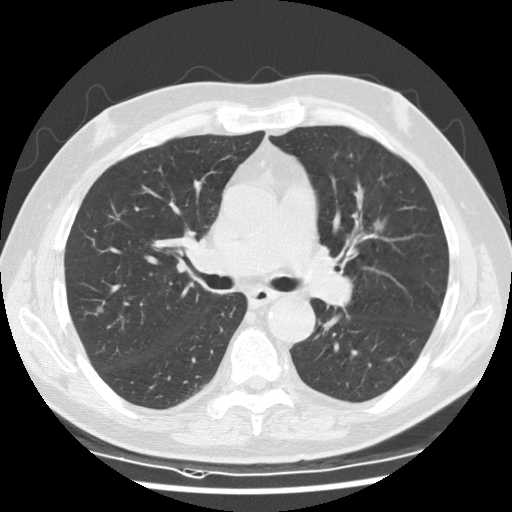
Low-dose screening chest CT, axial slice, baseline annual screen, lung window (W 1500 / L -600 HU). Male participant, aged 73 years at enrolment. Current smoker at enrolment.
Expert-annotated lung lesion, bounding box <332,203,404,254> (left, top, right, bottom; pixels). The exam's reader record, not a measurement of the box and not confirmed to be the same lesion: non-calcified nodule or mass ≥4 mm, right lower lobe, 13 × 13 mm, smooth margins, soft tissue attenuation. Note: the box lies in the patient's left hemithorax on this image, whereas the reader's record names the right lung; they may be different findings. Lung cancer was diagnosed 307 days after this screen: adenocarcinoma, NOS, left upper lobe, poorly differentiated (G3), stage IA (AJCC 6th edition), 19 mm at pathology.